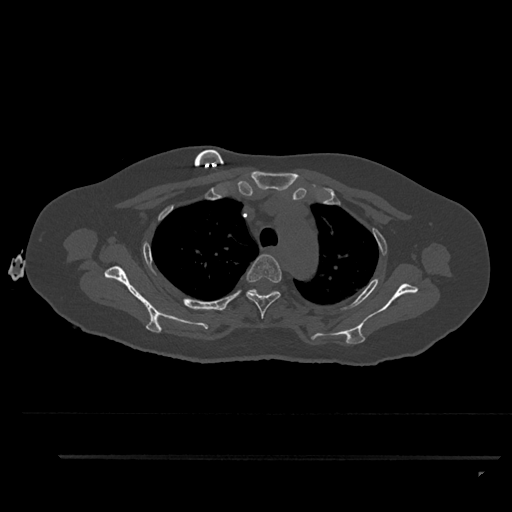
CT including the spine, one axial slice; slice 676 of 797 in the series (ordered by position); reconstruction kernel Br40s/3; 120 kVp; bone window (W 1800 / L 400 HU); 512 × 512 image matrix, field of view 408 × 408 mm. Female patient, age 44 years. Case-level facts recorded for this patient, not image findings: primary cancer: renal; vertebrae with lytic lesions (as recorded): L1.
Outlined on this slice (semi-automatic segmentation, software-assisted and operator-edited):
- T3 vertebra: bounding box [x1, y1, x2, y2] px = [246, 254, 282, 319]
- T4 vertebra: [249, 289, 279, 295]